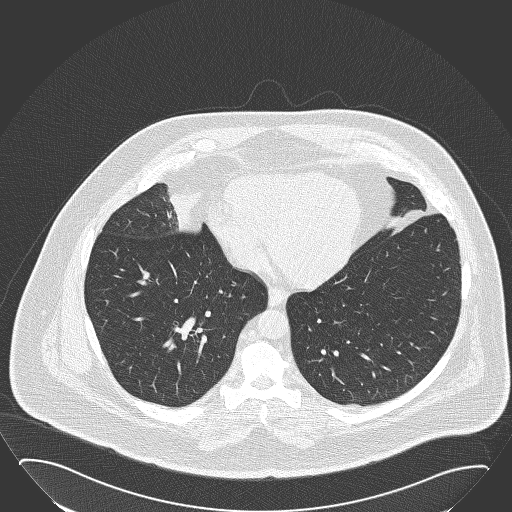
Low-dose screening chest CT, one axial slice; slice 59 of 168 in the series (ordered by position); reconstruction kernel B50f; lung window (W 1500 / L -600 HU); 2 mm slice thickness; 512 × 512 image matrix, field of view 432 × 432 mm.
Annotated regions visible in this slice (expert manual segmentation):
- lesion 1 (tumor, hilum of right lung): bounding box (x1, y1, x2, y2) in pixels: (167, 190, 204, 232)